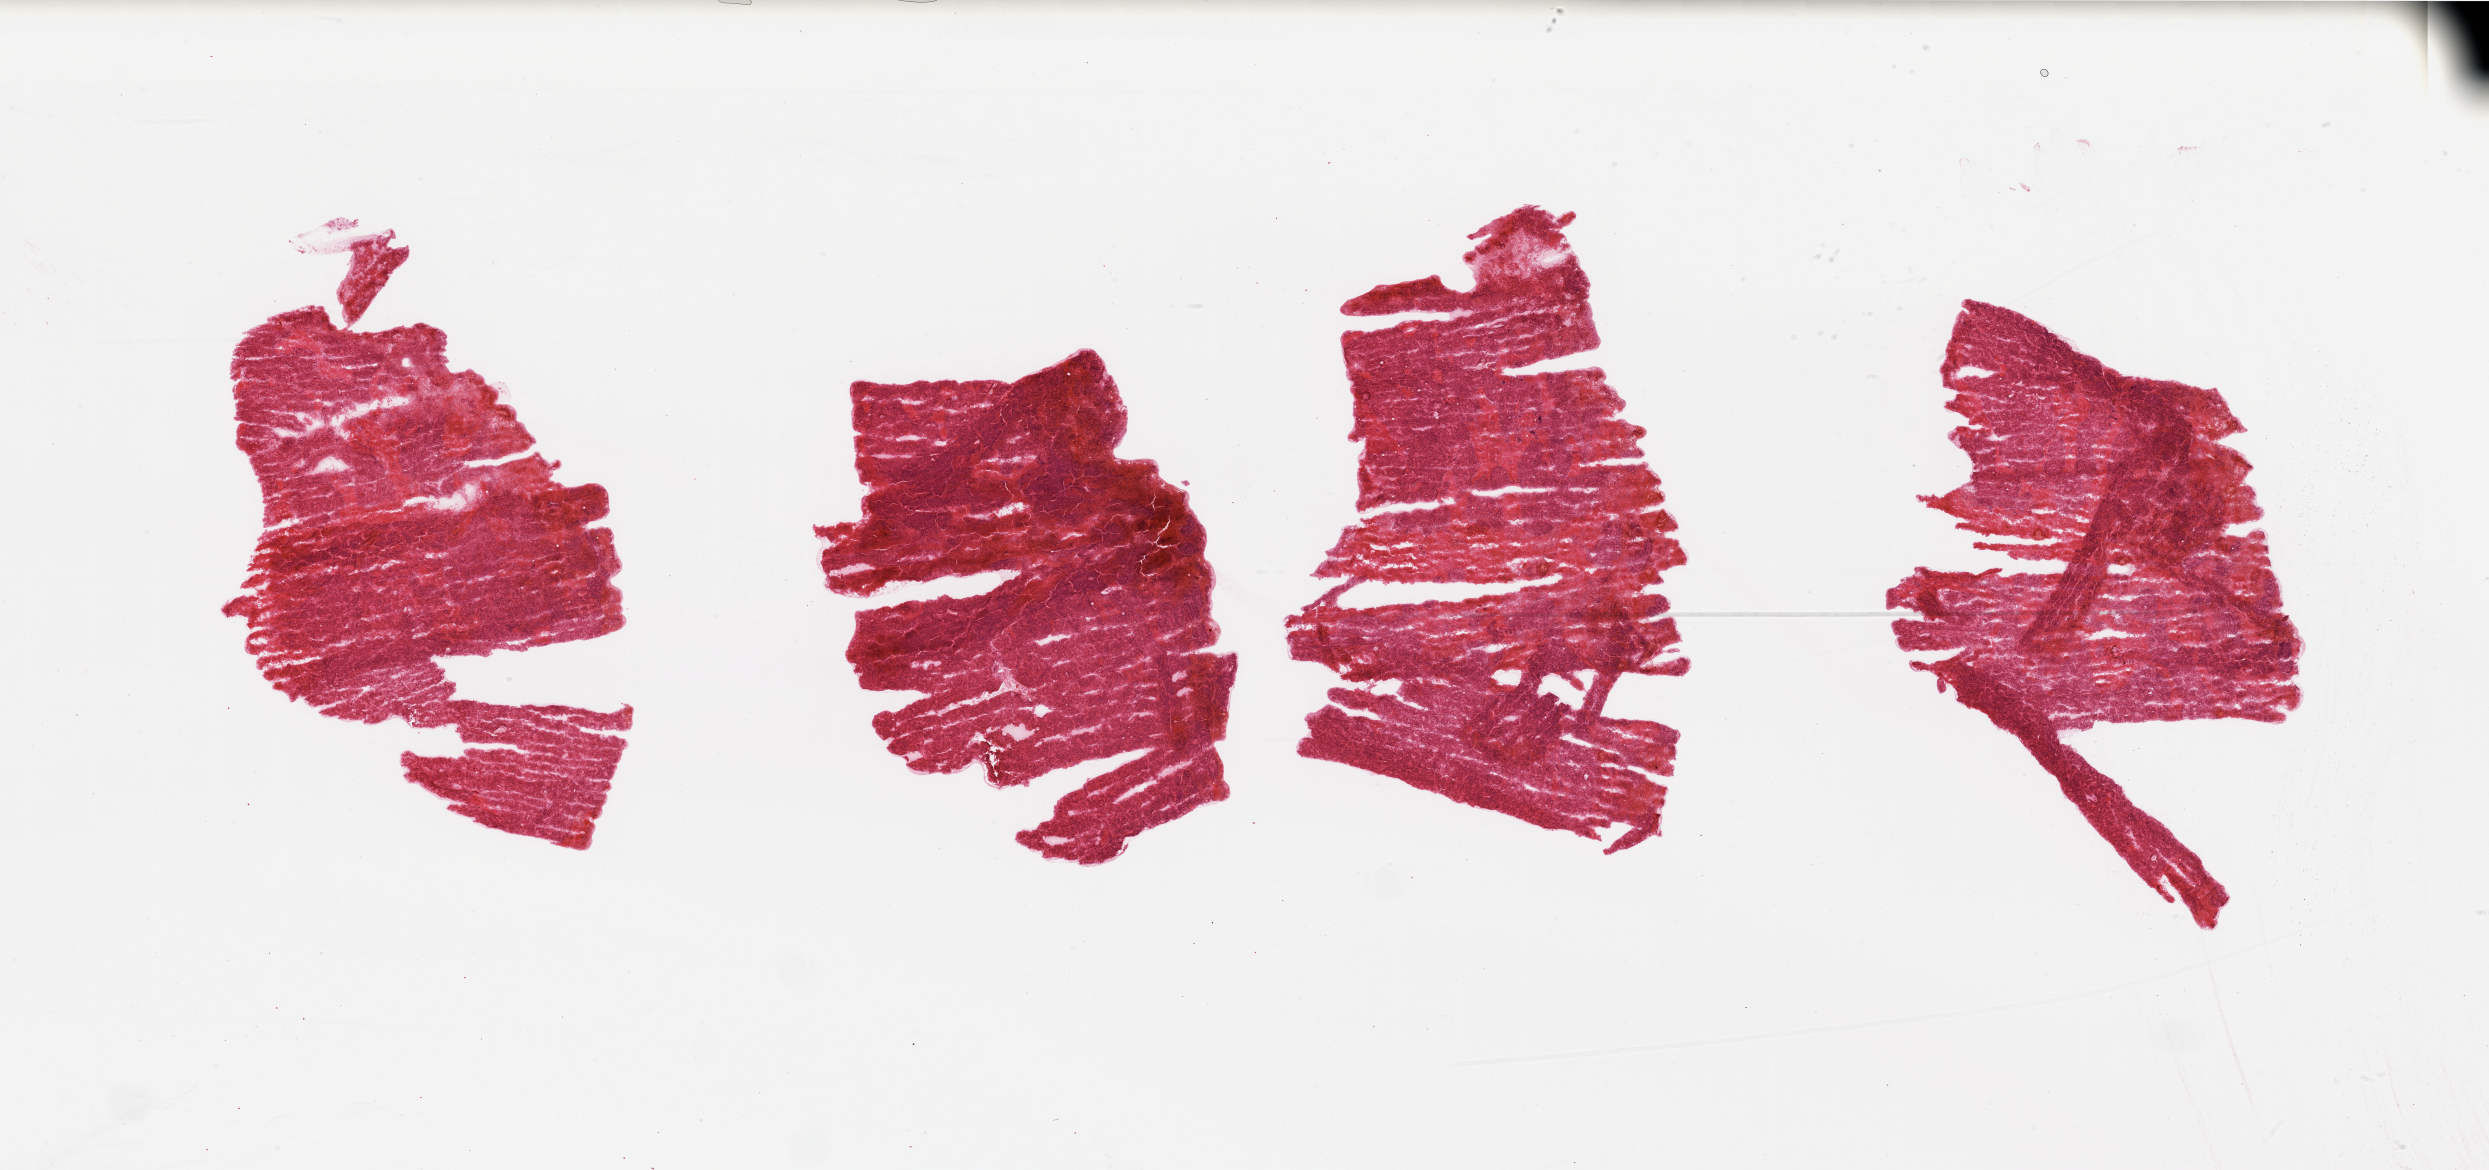
Whole-slide histology image, H&E-stained — shown as a low-resolution overview of the whole scanned area (about 39.4 x 18.5 mm, slide scanned at 20x); tumour tissue sample, kidney. Female, 49 y/o. Histologic grade: G3 (poorly differentiated).
Histologic diagnosis: Renal cell carcinoma, NOS. AJCC pathologic stage: II.